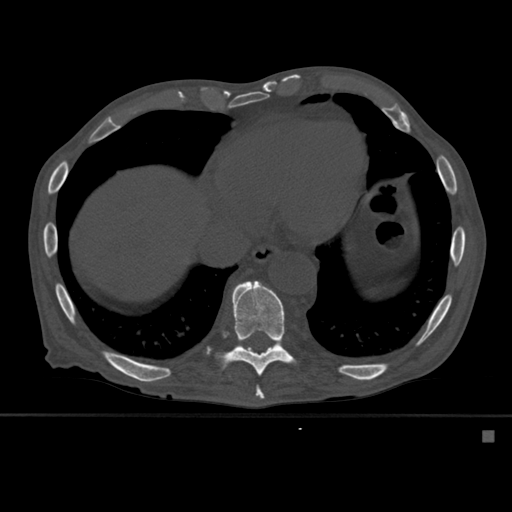
CT including the spine, one axial slice. Bone window (W 1800 / L 400 HU). 1.5 mm slice thickness. 512 × 512 image matrix. Patient: male, 78 years. Case-level facts recorded for this patient, not image findings: primary cancer: prostate.
Annotated regions visible in this slice (semi-automatic segmentation, software-assisted and operator-edited):
- T10 vertebra: bounding box (x1, y1, x2, y2) in pixels: (207, 280, 296, 377)
- T9 vertebra: (256, 386, 264, 399)